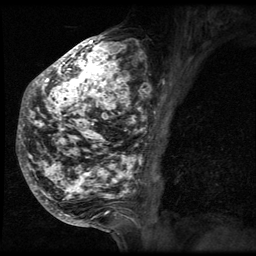
Breast MRI (dynamic contrast-enhanced), one sagittal slice; position 27 of 64 along the scan axis; 3 images stored at this slice position (order not interpretable as contrast timing); 1.5 T; TE 4.2 ms, TR 9 ms; 2.5 mm slice thickness; 256 × 256 image matrix, field of view 180 × 180 mm. Patient: female, 50 years. Case-level facts recorded for this patient, not image findings: setting: breast cancer imaged before/during neoadjuvant chemotherapy; receptor status: triple-negative.
Annotated regions visible in this slice (semi-automatically segmented with operator editing):
- analysis volume of interest (the breast-tissue region the enhancement analysis was run in; not a lesion): box from (x=24, y=39) to (x=151, y=212) px
- tumour enhancement mask (voxels above the 140 % enhancement threshold inside the analysis volume of interest): (x=24, y=39)–(x=151, y=199)